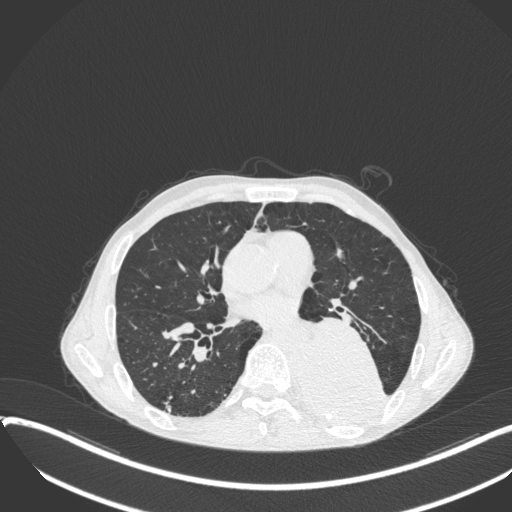
Chest CT, one axial slice. Slice 184 of 400 in the series (ordered by position). Lung window (W 1500 / L -600 HU). 512 × 512 image matrix, field of view 400 × 400 mm. Male patient, age 57 years. Case-level facts recorded for this patient, not image findings: clinical TNM (as recorded): T4 N0 M0.
Structures marked on this image (bounding box drawn by a radiologist):
- lung tumour (recorded histology: squamous cell carcinoma): box from (x=295, y=311) to (x=390, y=424) px